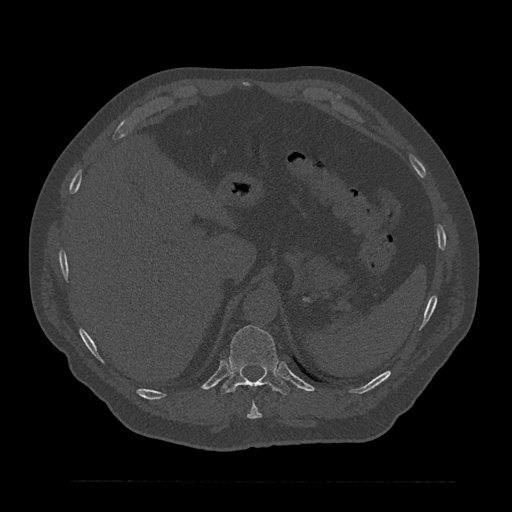
CT including the spine, one axial slice; position 307 of 797 along the scan axis; reconstruction kernel Br40s/3; 120 kVp; bone window (W 1800 / L 400 HU); 512 × 512 image matrix, field of view 430 × 430 mm. Male patient, age 61 years. Case-level facts recorded for this patient, not image findings: primary cancer: prostate.
Structures marked on this image (semi-automatic segmentation, software-assisted and operator-edited):
- T10 vertebra: bounding box <247,403,262,419> (left, top, right, bottom; pixels)
- T11 vertebra: <220,325,290,396>